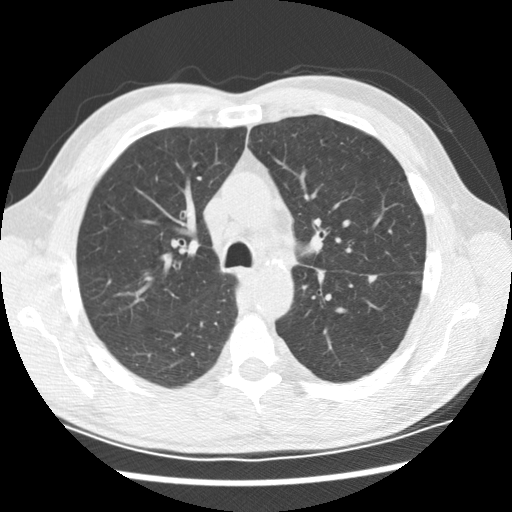
Low-dose screening chest CT, one axial slice; position 137 of 208 along the scan axis; reconstruction kernel STANDARD; lung window (W 1500 / L -600 HU); 2.5 mm slice thickness; 512 × 512 image matrix, field of view 340 × 340 mm.
Outlined on this slice (manually delineated by an expert):
- lesion 2 (tumor, lower lobe of left lung): bounding box (x1, y1, x2, y2) in pixels: (367, 275, 380, 285)